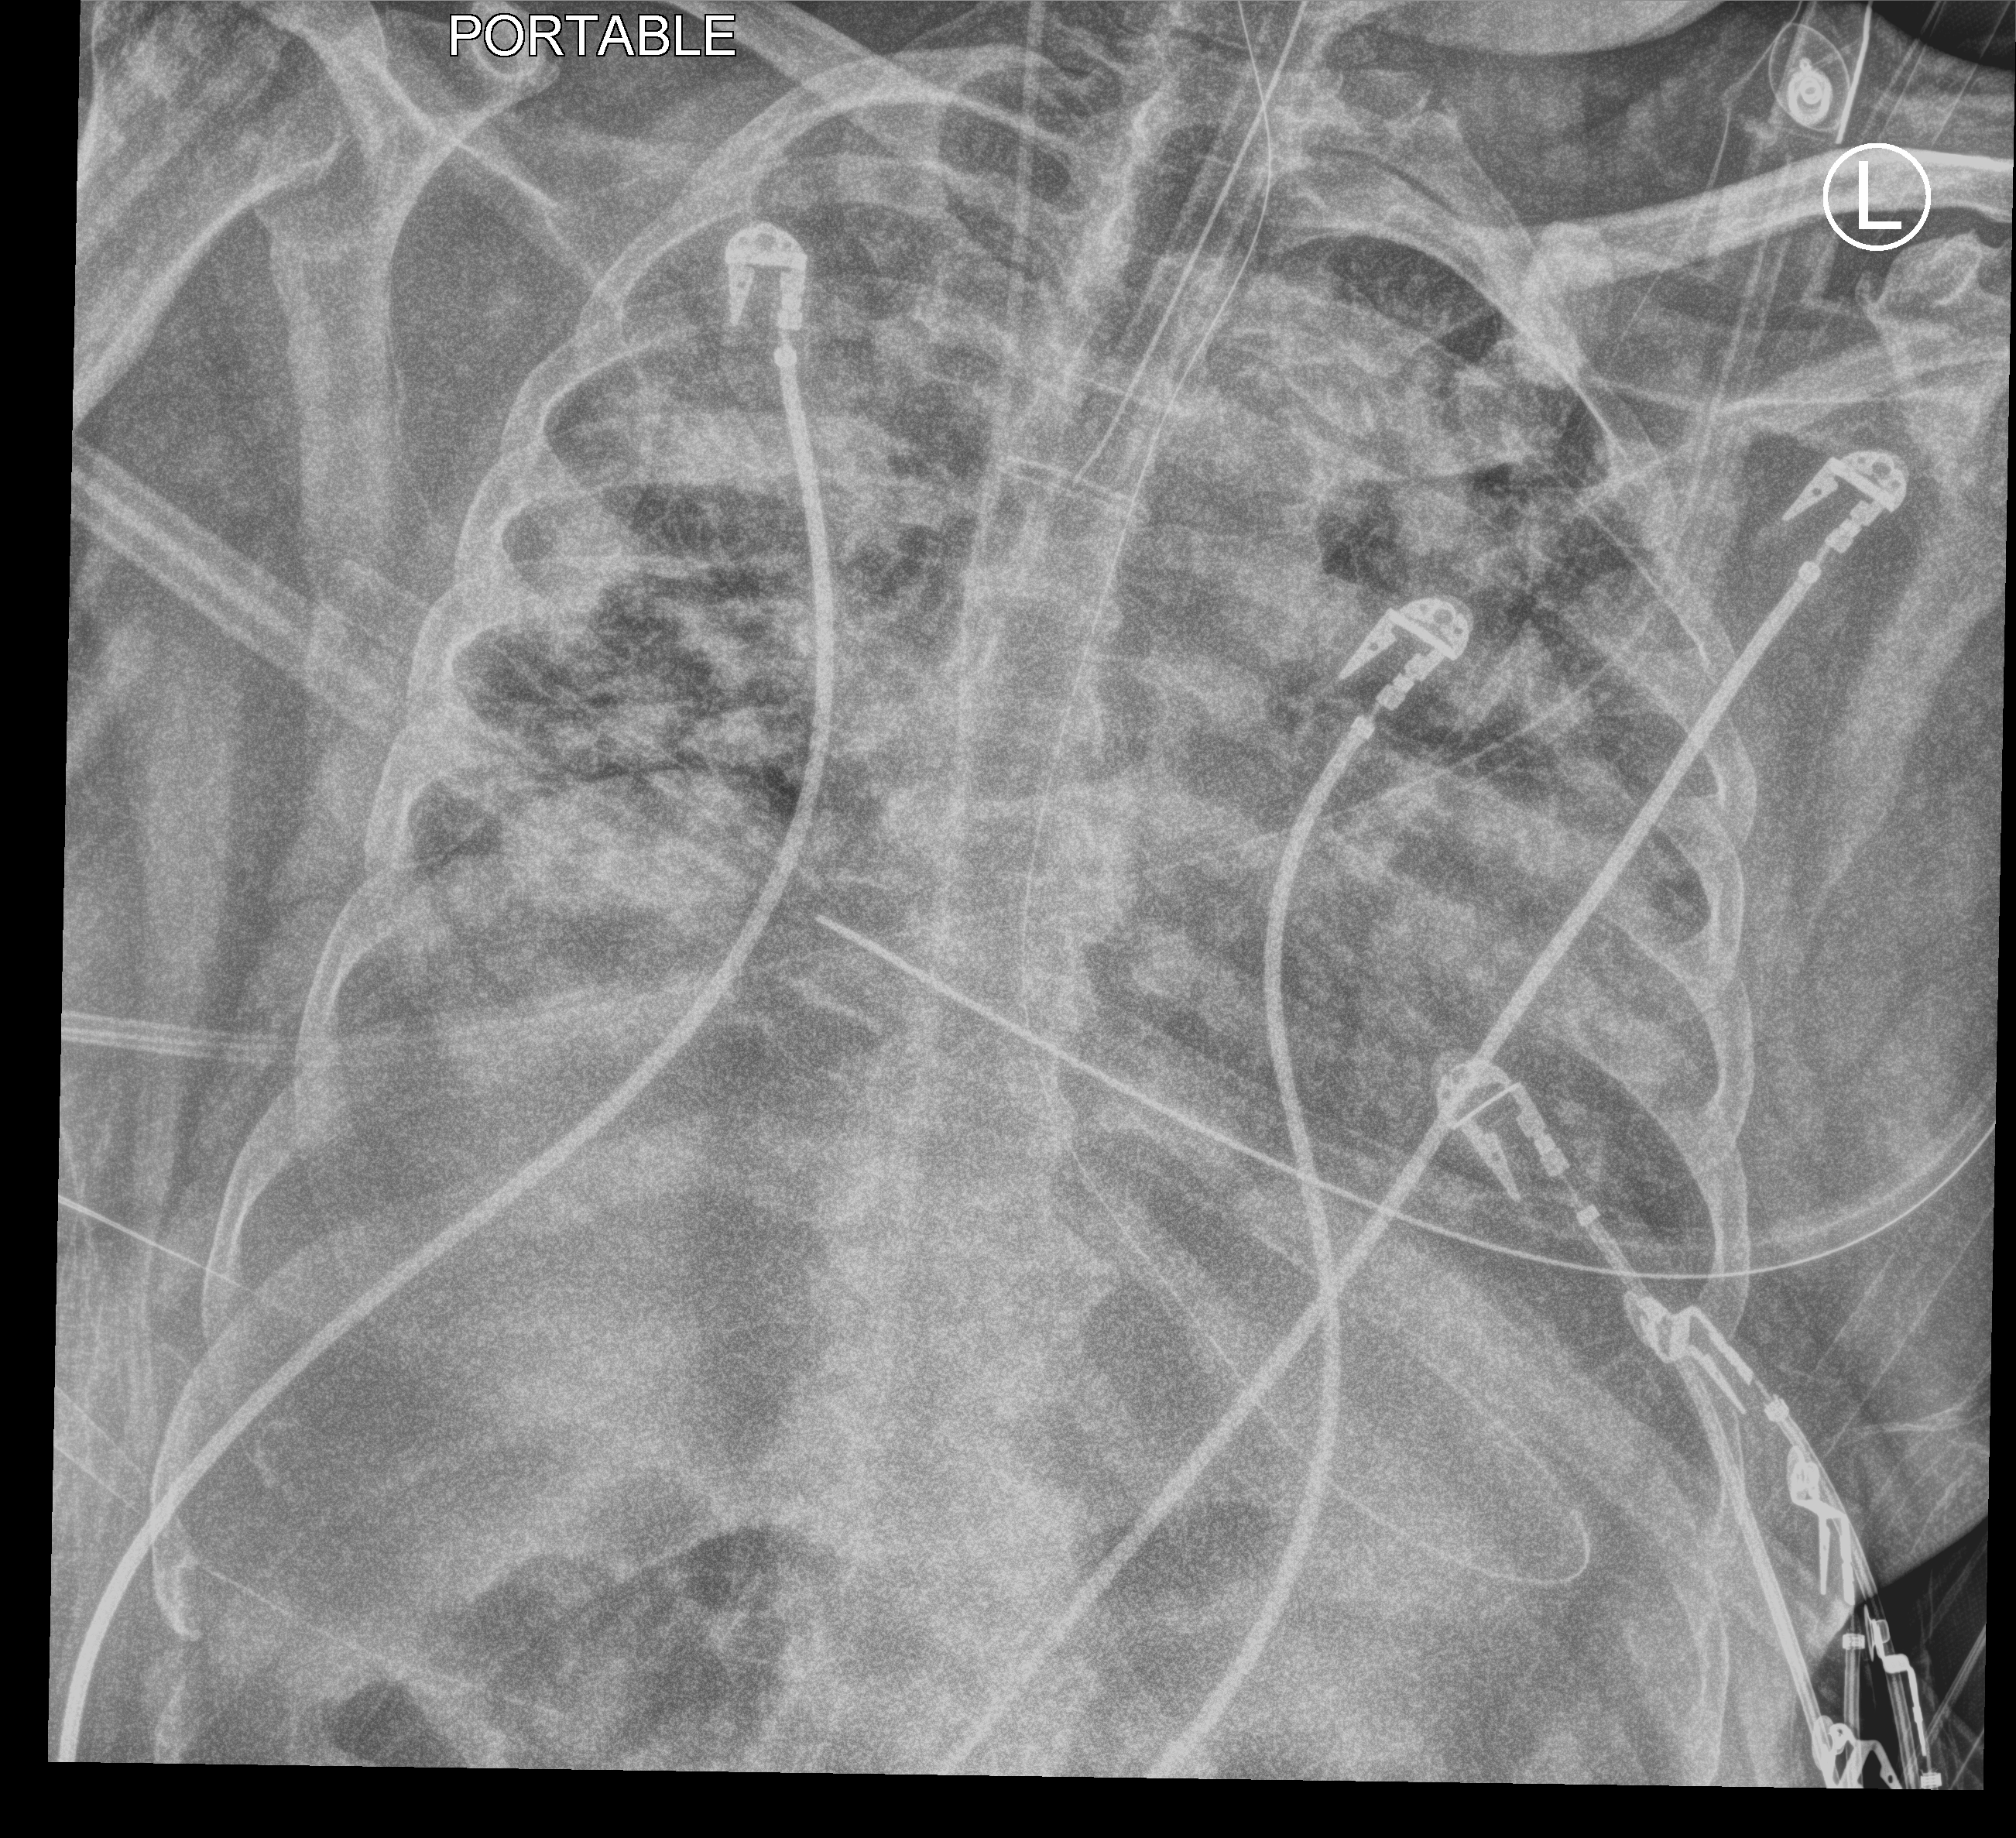
Portable chest radiograph, anteroposterior (AP) projection. Male patient hospitalised with COVID-19, age 60–74 years.
From the hospital-stay record, not from the radiograph (when in the stay this image was taken is not recorded):
- mechanically ventilated during this hospital stay: yes
- COPD (admission record): no